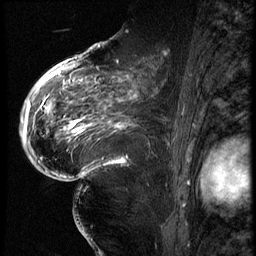
Breast MRI (dynamic contrast-enhanced), one sagittal slice. Slice 39 of 62 in the series (ordered by position). 3 images stored at this slice position (order not interpretable as contrast timing). 1.5 T. TE 4.2 ms, TR 9 ms. 2.5 mm slice thickness. 256 × 256 image matrix, field of view 180 × 180 mm. Patient: female, 56 years. From the clinical record (not read from this slice): setting: breast cancer imaged before/during neoadjuvant chemotherapy; receptor status: HER2-positive.
Structures marked on this image (semi-automatic segmentation, software-assisted and operator-edited):
- analysis volume of interest (the breast-tissue region the enhancement analysis was run in; not a lesion): bounding box <84,75,181,153> (left, top, right, bottom; pixels)
- tumour enhancement mask (voxels above the 140 % enhancement threshold inside the analysis volume of interest): <85,75,132,127>